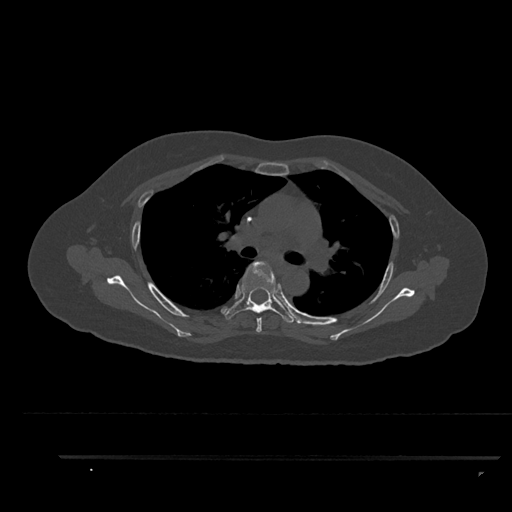
CT including the spine, one axial slice. Position 613 of 797 along the scan axis. Reconstruction kernel Br40s/3. 120 kVp. Bone window (W 1800 / L 400 HU). 0.5 mm slice thickness. 512 × 512 image matrix. Patient: female, 44 years. From the clinical record (not read from this slice): primary cancer: renal.
Structures marked on this image (semi-automatically segmented with operator editing):
- T4 vertebra: box from (x=256, y=317) to (x=262, y=333) px
- T5 vertebra: (x=221, y=261)–(x=296, y=323)